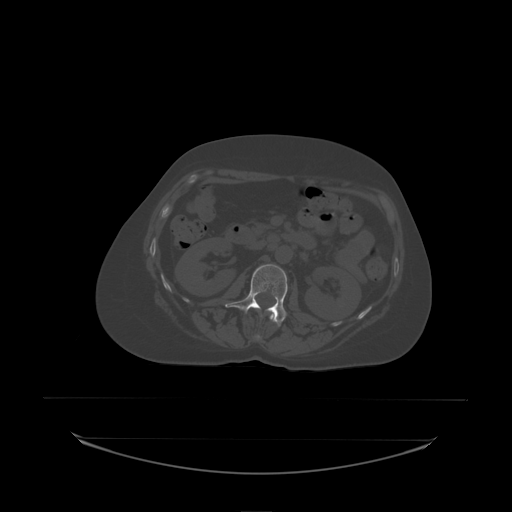
CT including the spine, one axial slice; slice 74 of 242 in the series (ordered by position); bone window (W 1800 / L 400 HU); 512 × 512 image matrix, field of view 500 × 500 mm. Patient: female, 53 years. From the clinical record (not read from this slice): primary cancer: lung; vertebrae with lytic lesions (as recorded): T7, L1.
Structures marked on this image (semi-automatically segmented with operator editing):
- L1 vertebra: bounding box [x1, y1, x2, y2] px = [256, 313, 275, 338]
- L2 vertebra: [226, 264, 288, 327]